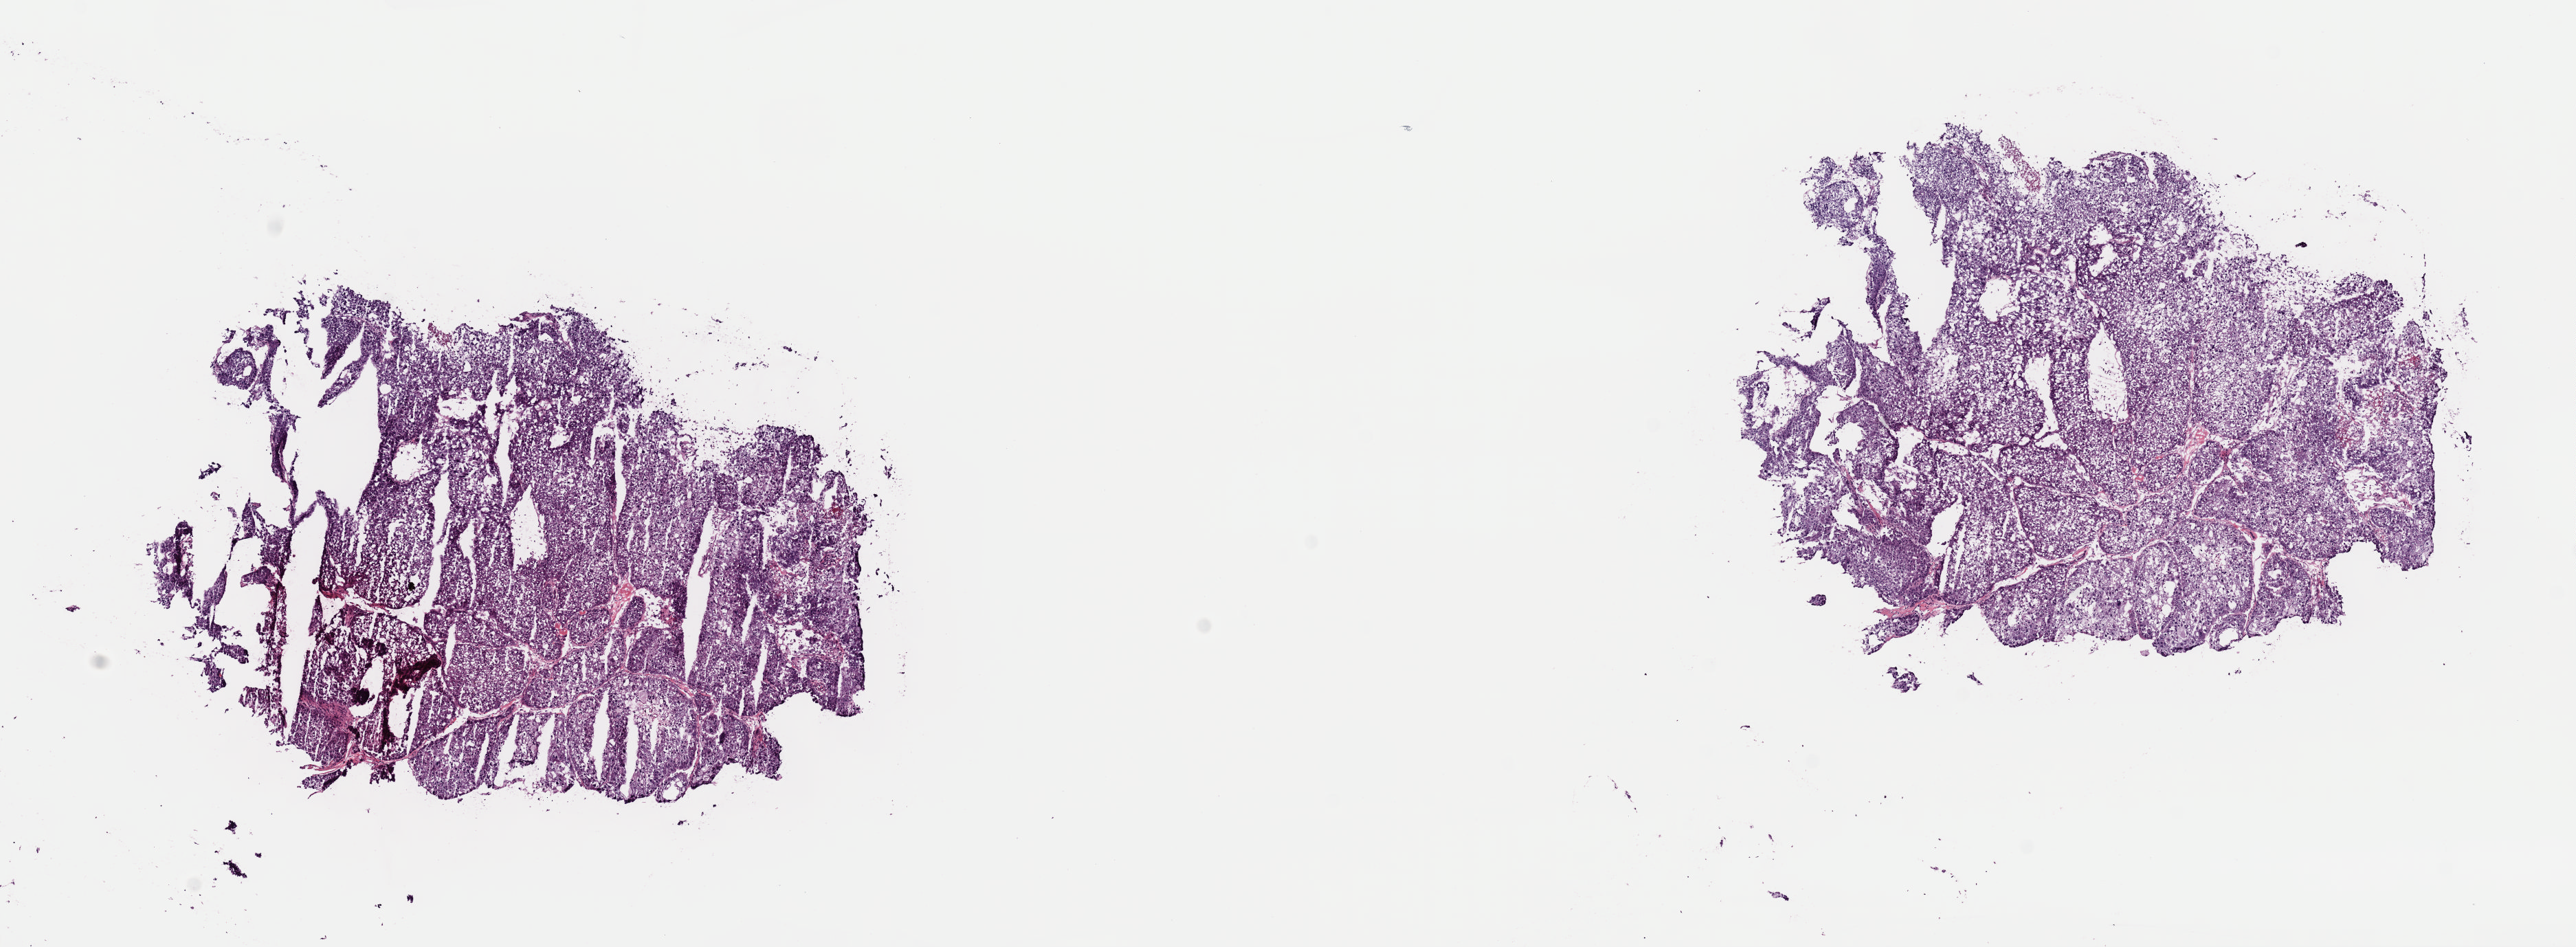
Hematoxylin and eosin (H&E) stained whole-slide image, shown as a low-resolution overview of the whole scanned area (about 14.8 x 5.4 mm), frozen section from the top of the tissue portion, liver, primary tumour sample. Male patient; age at initial diagnosis 61 years.
Histologic diagnosis: Hepatocellular carcinoma, NOS.